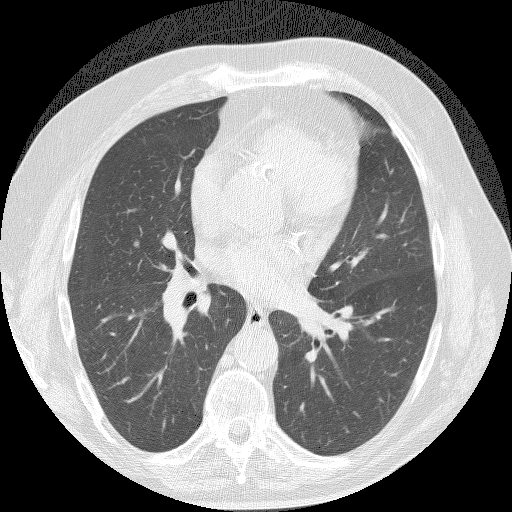
Axial slice from a low-dose chest CT screening exam, baseline annual screen, lung window (W 1500 / L -600 HU), 2.5 mm slice thickness, lung (sharp) reconstruction kernel (BONE), 512 × 512 image matrix. Male participant, aged 61 years at enrolment. Current smoker at enrolment.
Expert-annotated lung lesion, box from (x=111, y=228) to (x=156, y=265) px. The screening reader recorded 3 non-calcified nodules or masses ≥4 mm on this exam (right upper lobe, right lower lobe); which of them this box marks is not recorded. Later outcome: lung cancer diagnosed 491 days after this screen — bronchiolo-alveolar adenocarcinoma, NOS, right middle lobe, well differentiated (G1), stage IA (AJCC 6th edition), 15 mm at pathology.